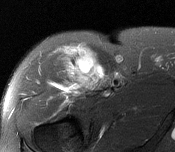
MRI of an extremity soft-tissue mass, one axial slice; position 111 of 116 along the scan axis; T2-weighted fat-saturated; MR volume resampled by the dataset authors to the PET/CT grid (not the native acquisition matrix); 3.27 mm slice thickness; 175 × 152 image matrix, field of view 171 × 148 mm. Male patient. From the clinical record (not read from this slice): histological type: pleiomorphic leiomyosarcoma; grade: intermediate; site of the primary tumour: right thigh.
Annotated regions visible in this slice (expert contour drawn on MRI and transferred to this co-registered scan by the dataset authors):
- gross tumour volume including surrounding oedema: bounding box (x1, y1, x2, y2) in pixels: (67, 52, 103, 91)
- gross tumour volume (mass): (83, 63, 102, 87)